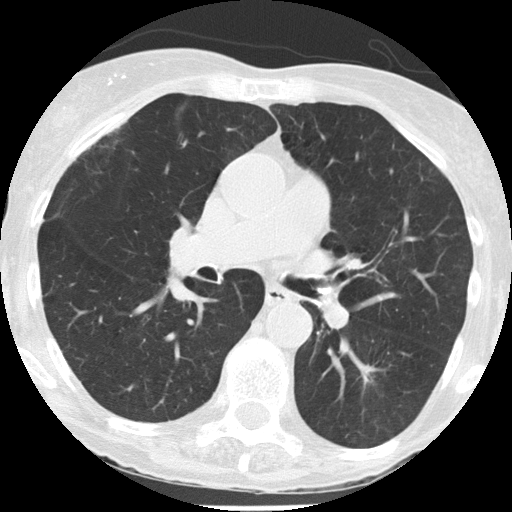
Low-dose screening chest CT, one axial slice; position 74 of 146 along the scan axis; reconstruction kernel FC51; lung window (W 1500 / L -600 HU); 512 × 512 image matrix, field of view 273 × 273 mm.
Structures marked on this image (expert manual segmentation):
- lesion 1 (tumor, lower lobe of left lung): box from (x=365, y=365) to (x=375, y=378) px